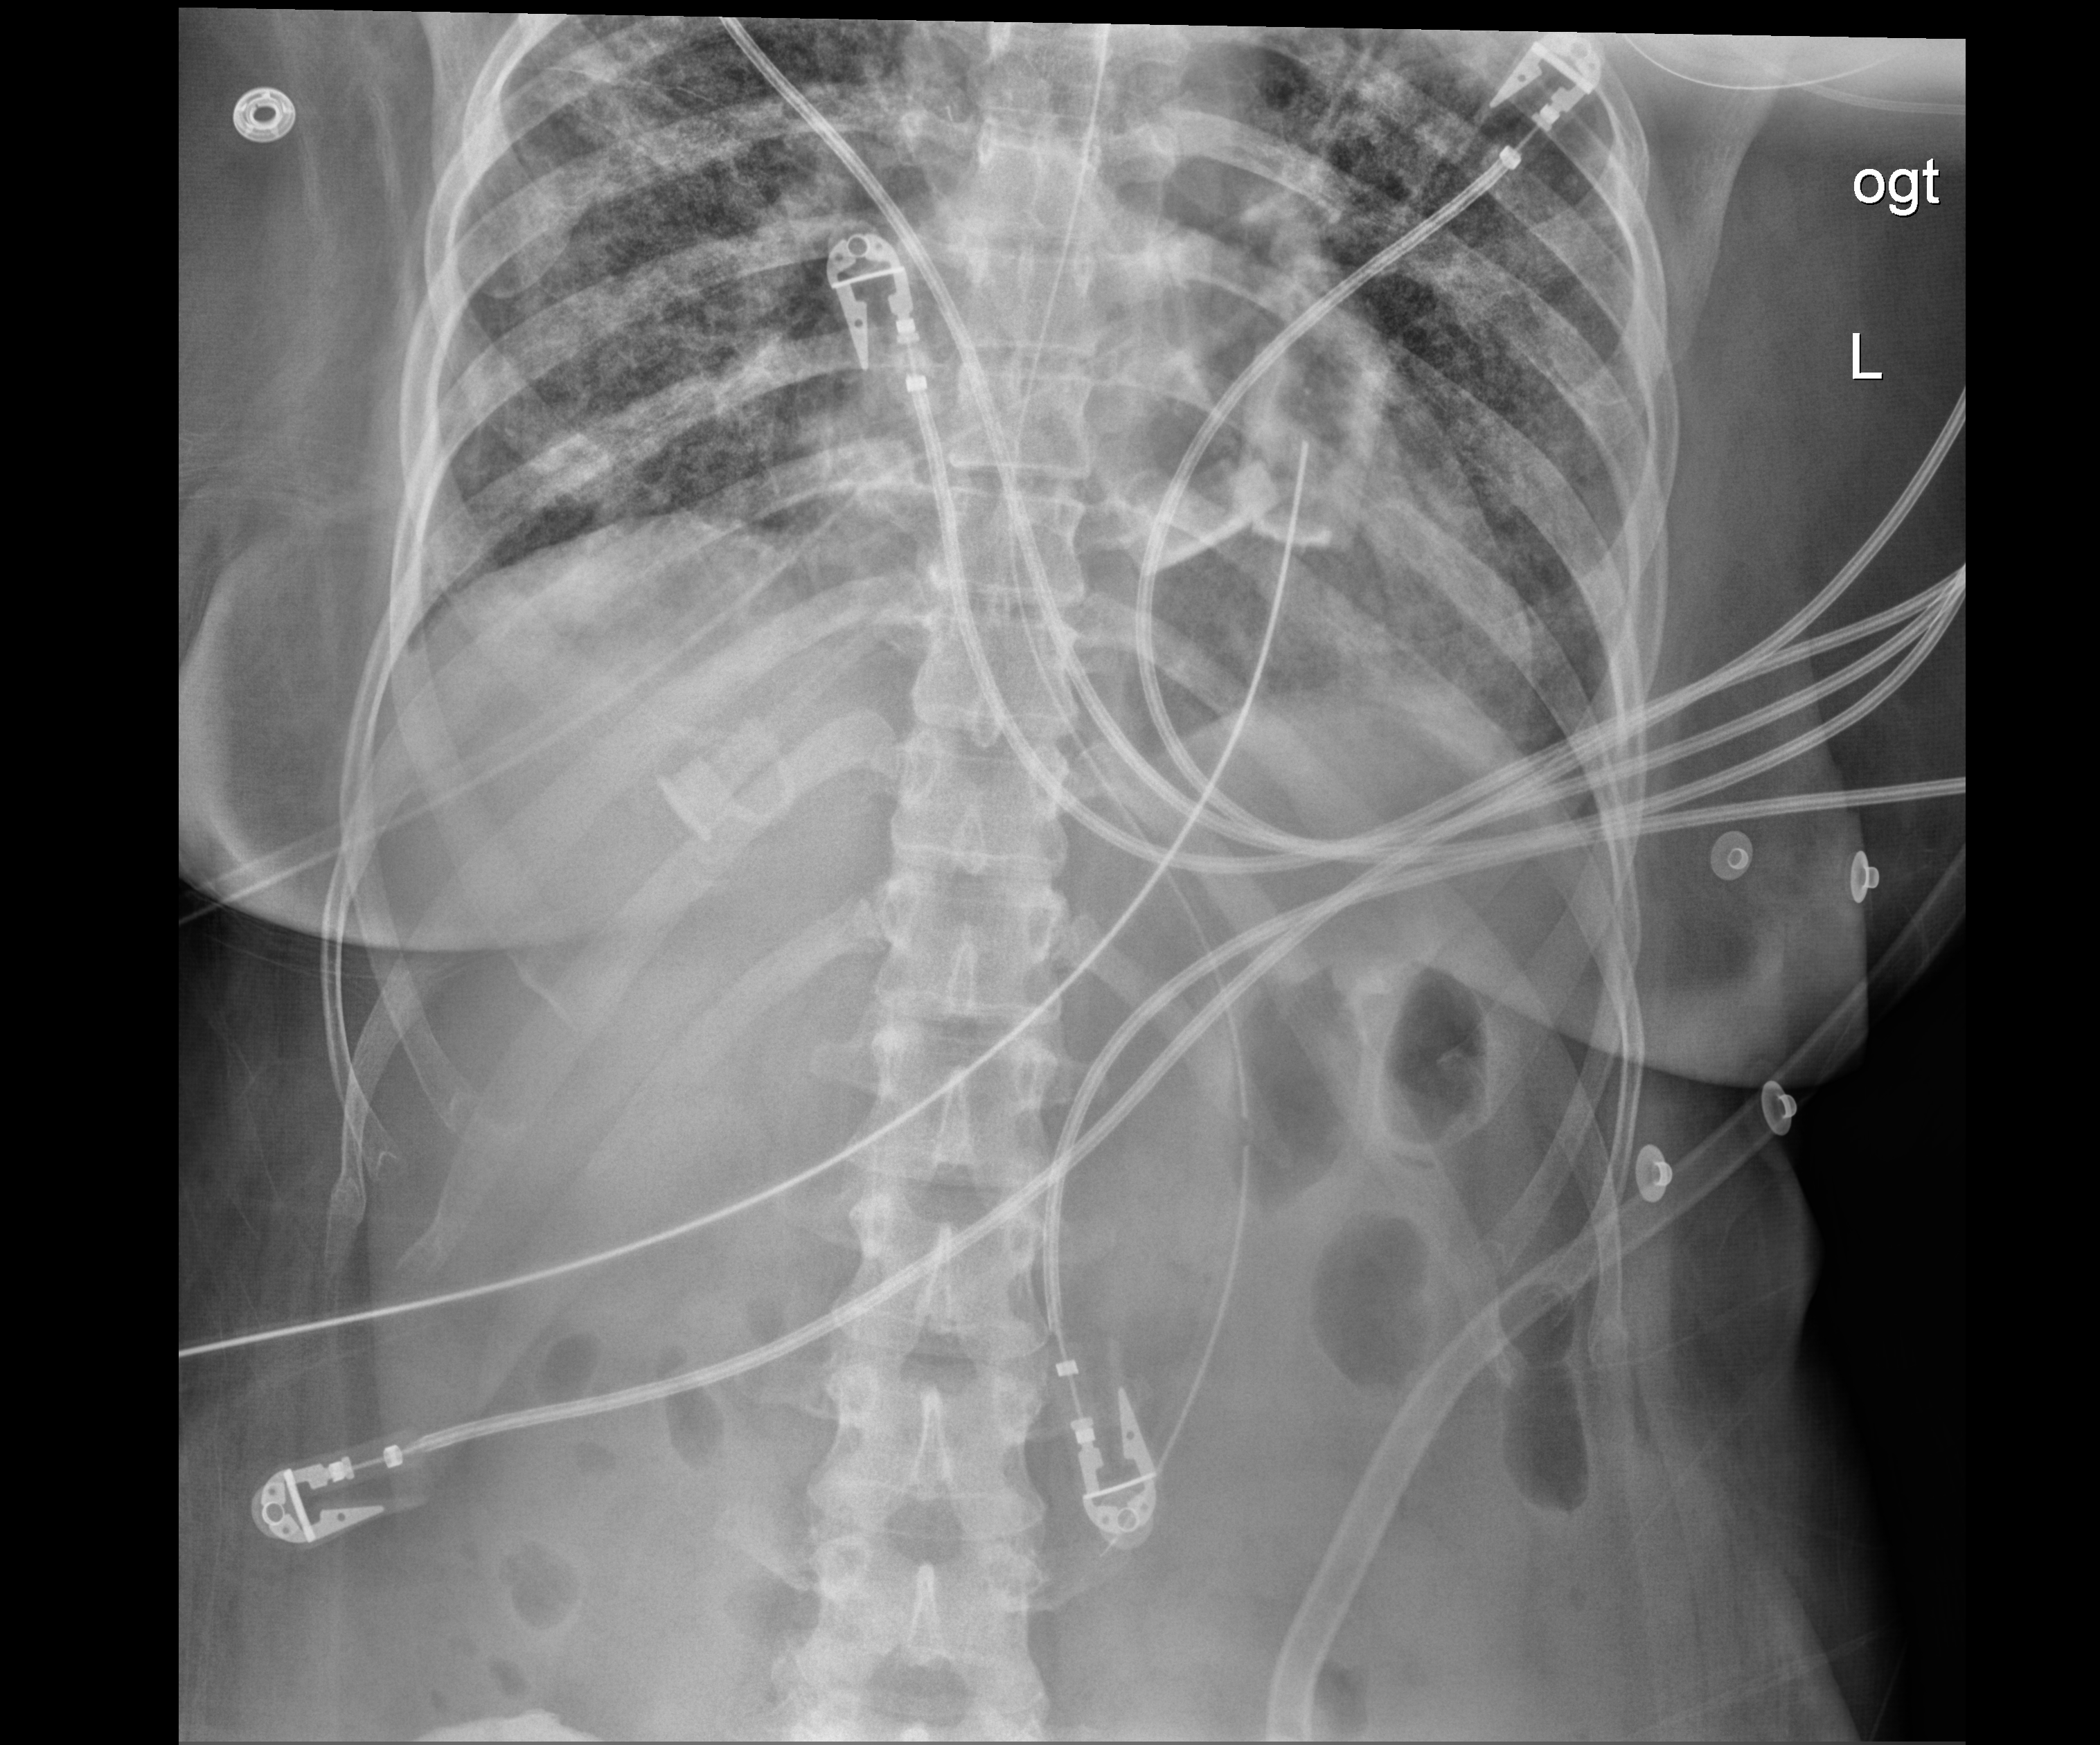
Portable chest radiograph, anteroposterior (AP) projection. Male patient hospitalised with COVID-19, age 18–59 years.
From the hospital-stay record, not from the radiograph (when in the stay this image was taken is not recorded): admitted to intensive care during this hospital stay: yes.